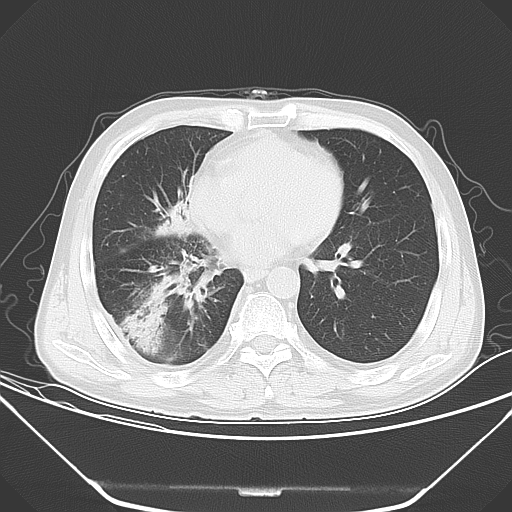
Chest CT, one axial slice; 120 kVp; lung window (W 1500 / L -600 HU); 5 mm slice thickness; 512 × 512 image matrix, field of view 379 × 379 mm. Patient: male, 54 years. Case-level facts recorded for this patient, not image findings: clinical TNM (as recorded): T2 N1 M0; histopathological grade: G3.
Annotated regions visible in this slice (bounding box drawn by a radiologist):
- lung tumour (recorded histology: adenocarcinoma): bounding box <117,285,167,356> (left, top, right, bottom; pixels)